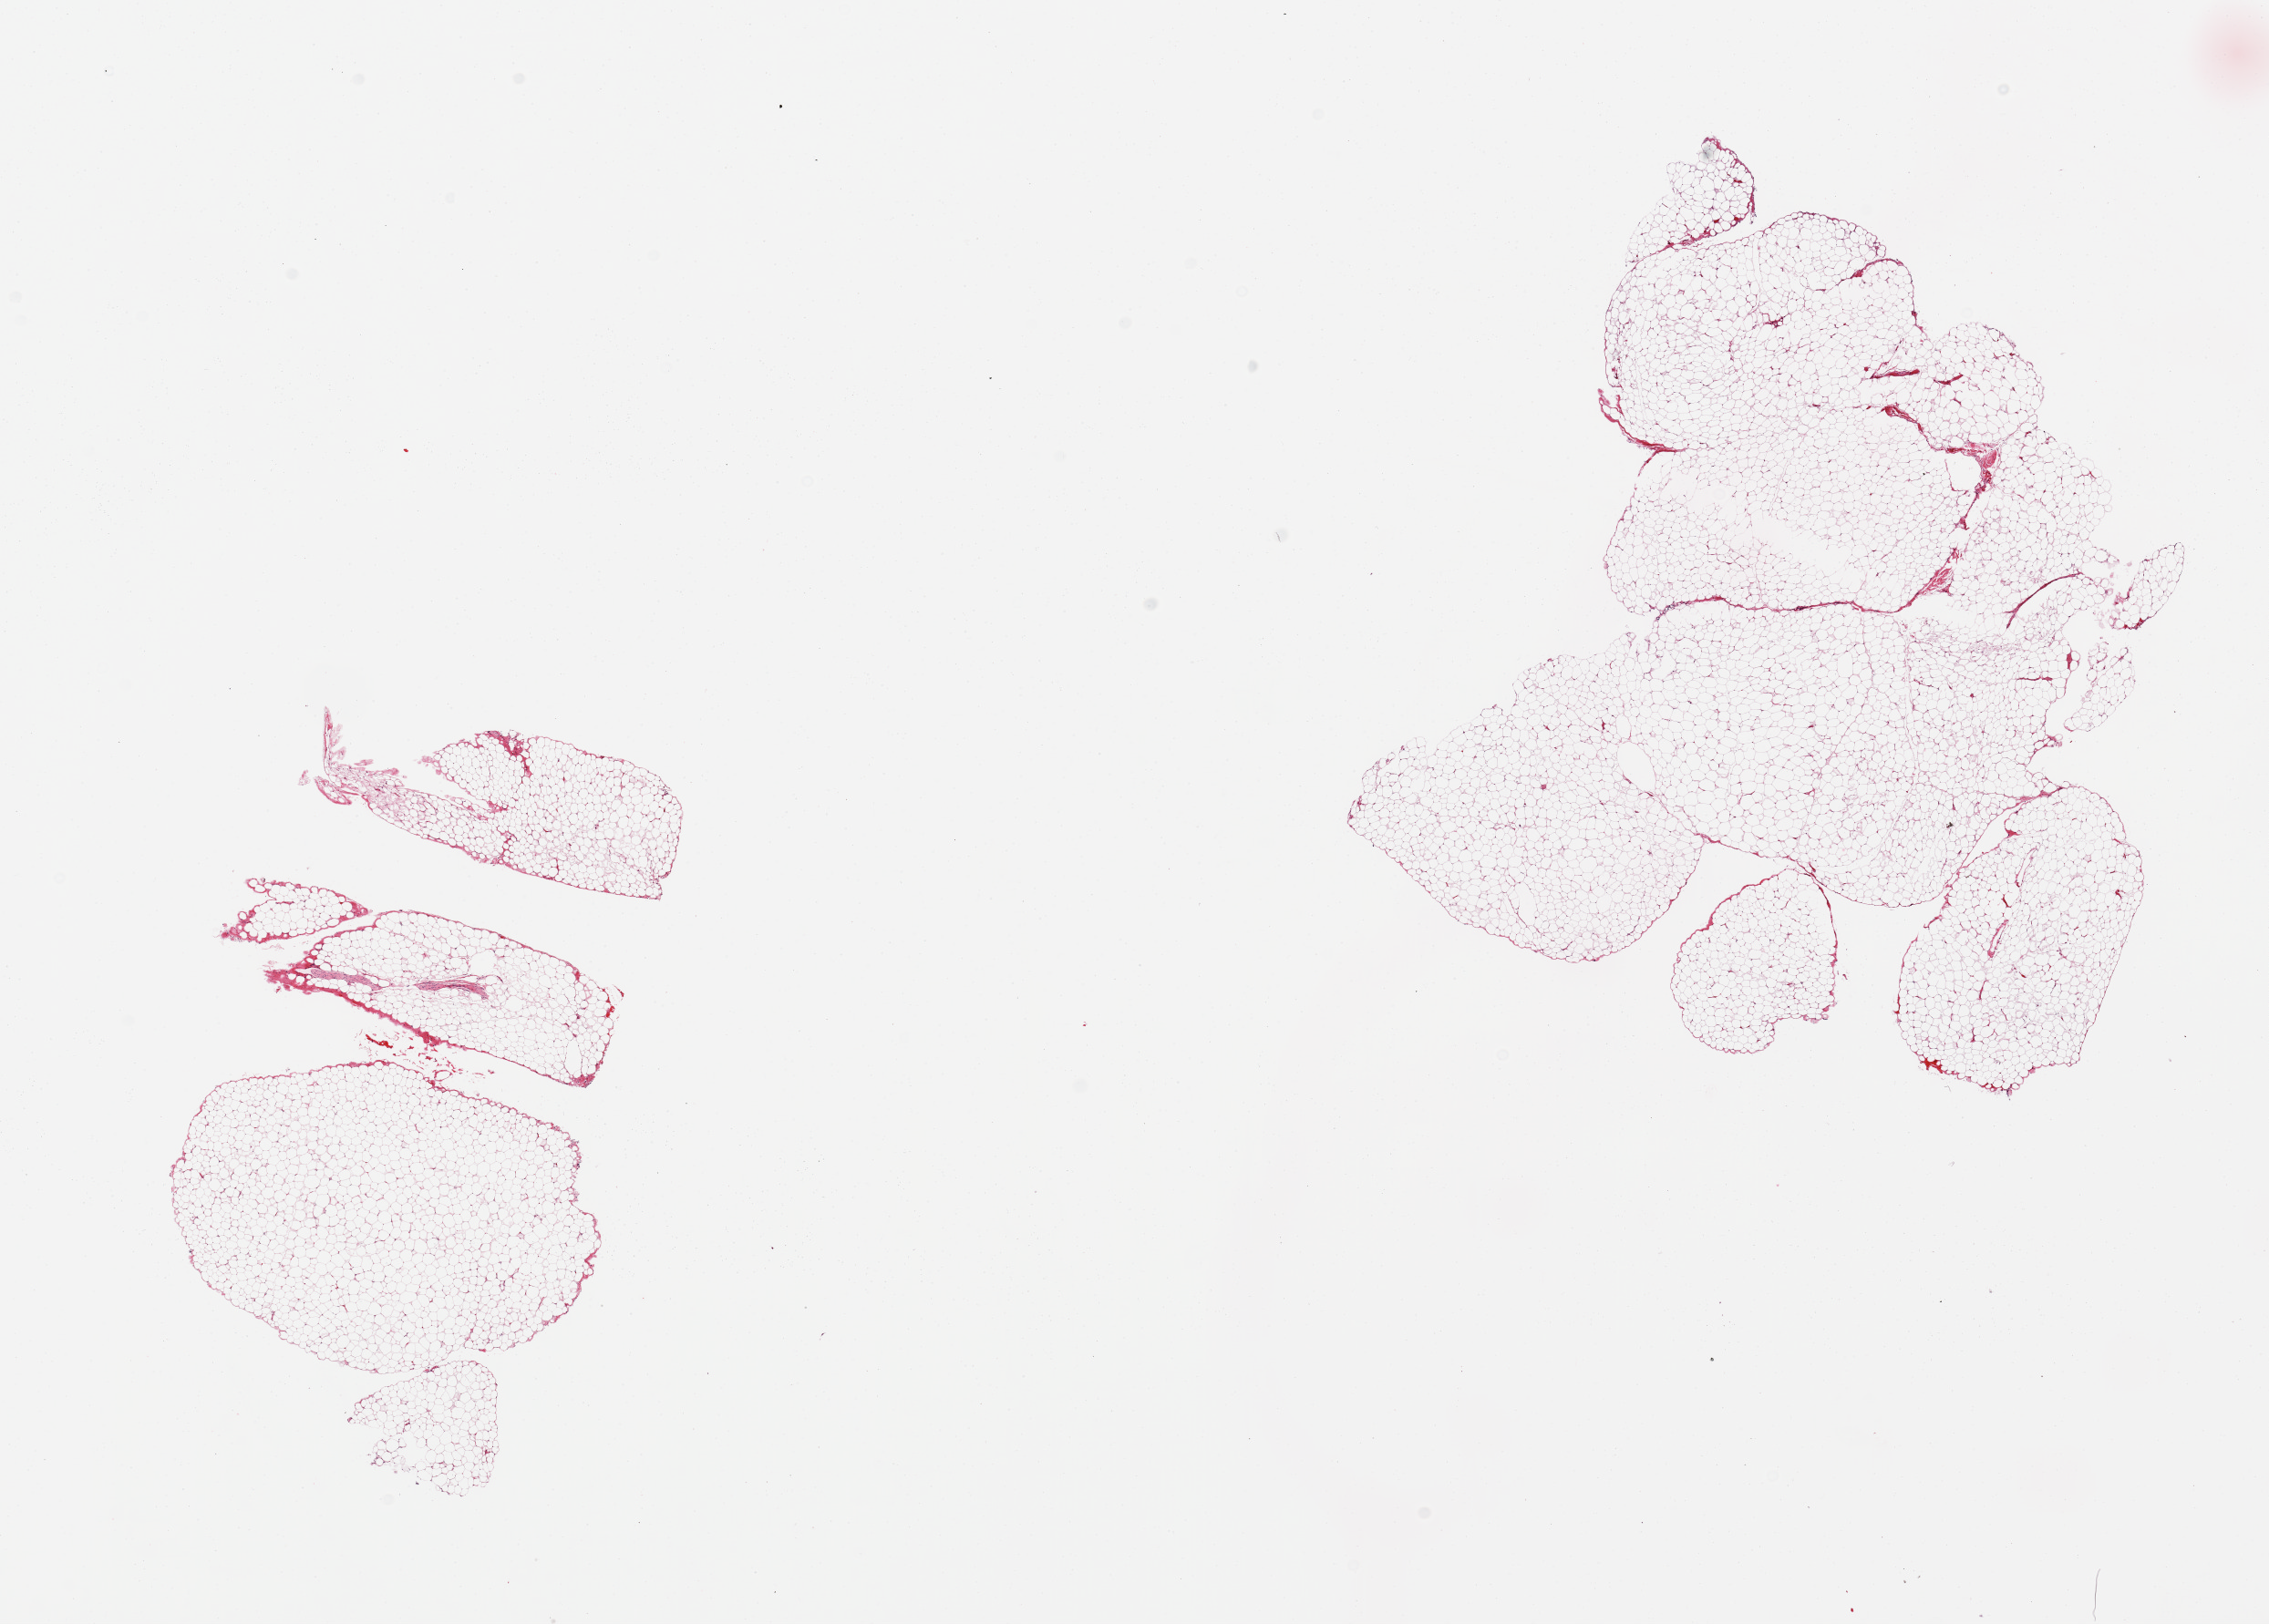
Digitized haematoxylin and eosin-stained section — low-resolution overview of the scanned area, about 19.7 x 14.1 mm (slide scanned at 20x); PAXgene-fixed paraffin-embedded (PFPE) section; sampled site (target tissue): omentum; donor tissue sample. Donor sex: female.
• review note (as recorded): 2 pieces, minimal vascular tissue/mesothelial hyperplasia